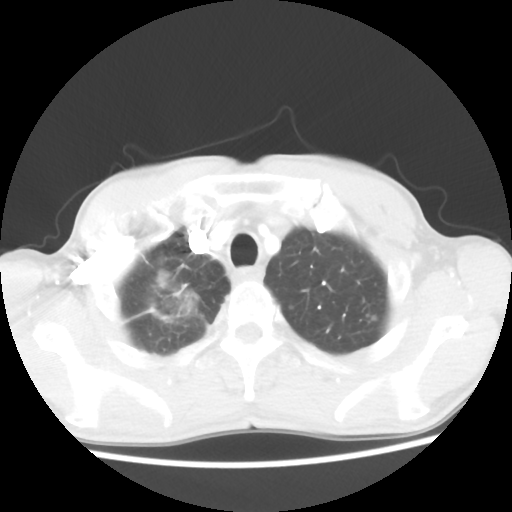
Chest CT, one axial slice; position 46 of 52 along the scan axis; reconstruction kernel STANDARD; 100 kVp; lung window (W 1500 / L -600 HU); 5 mm slice thickness; 512 × 512 image matrix, field of view 323 × 323 mm. Patient: male, 66 years. Case-level facts recorded for this patient, not image findings: clinical TNM (as recorded): T2 N0 M1a.
Annotated regions visible in this slice (bounding box drawn by a radiologist):
- lung tumour (recorded histology: adenocarcinoma): bounding box (x1, y1, x2, y2) in pixels: (139, 259, 203, 327)